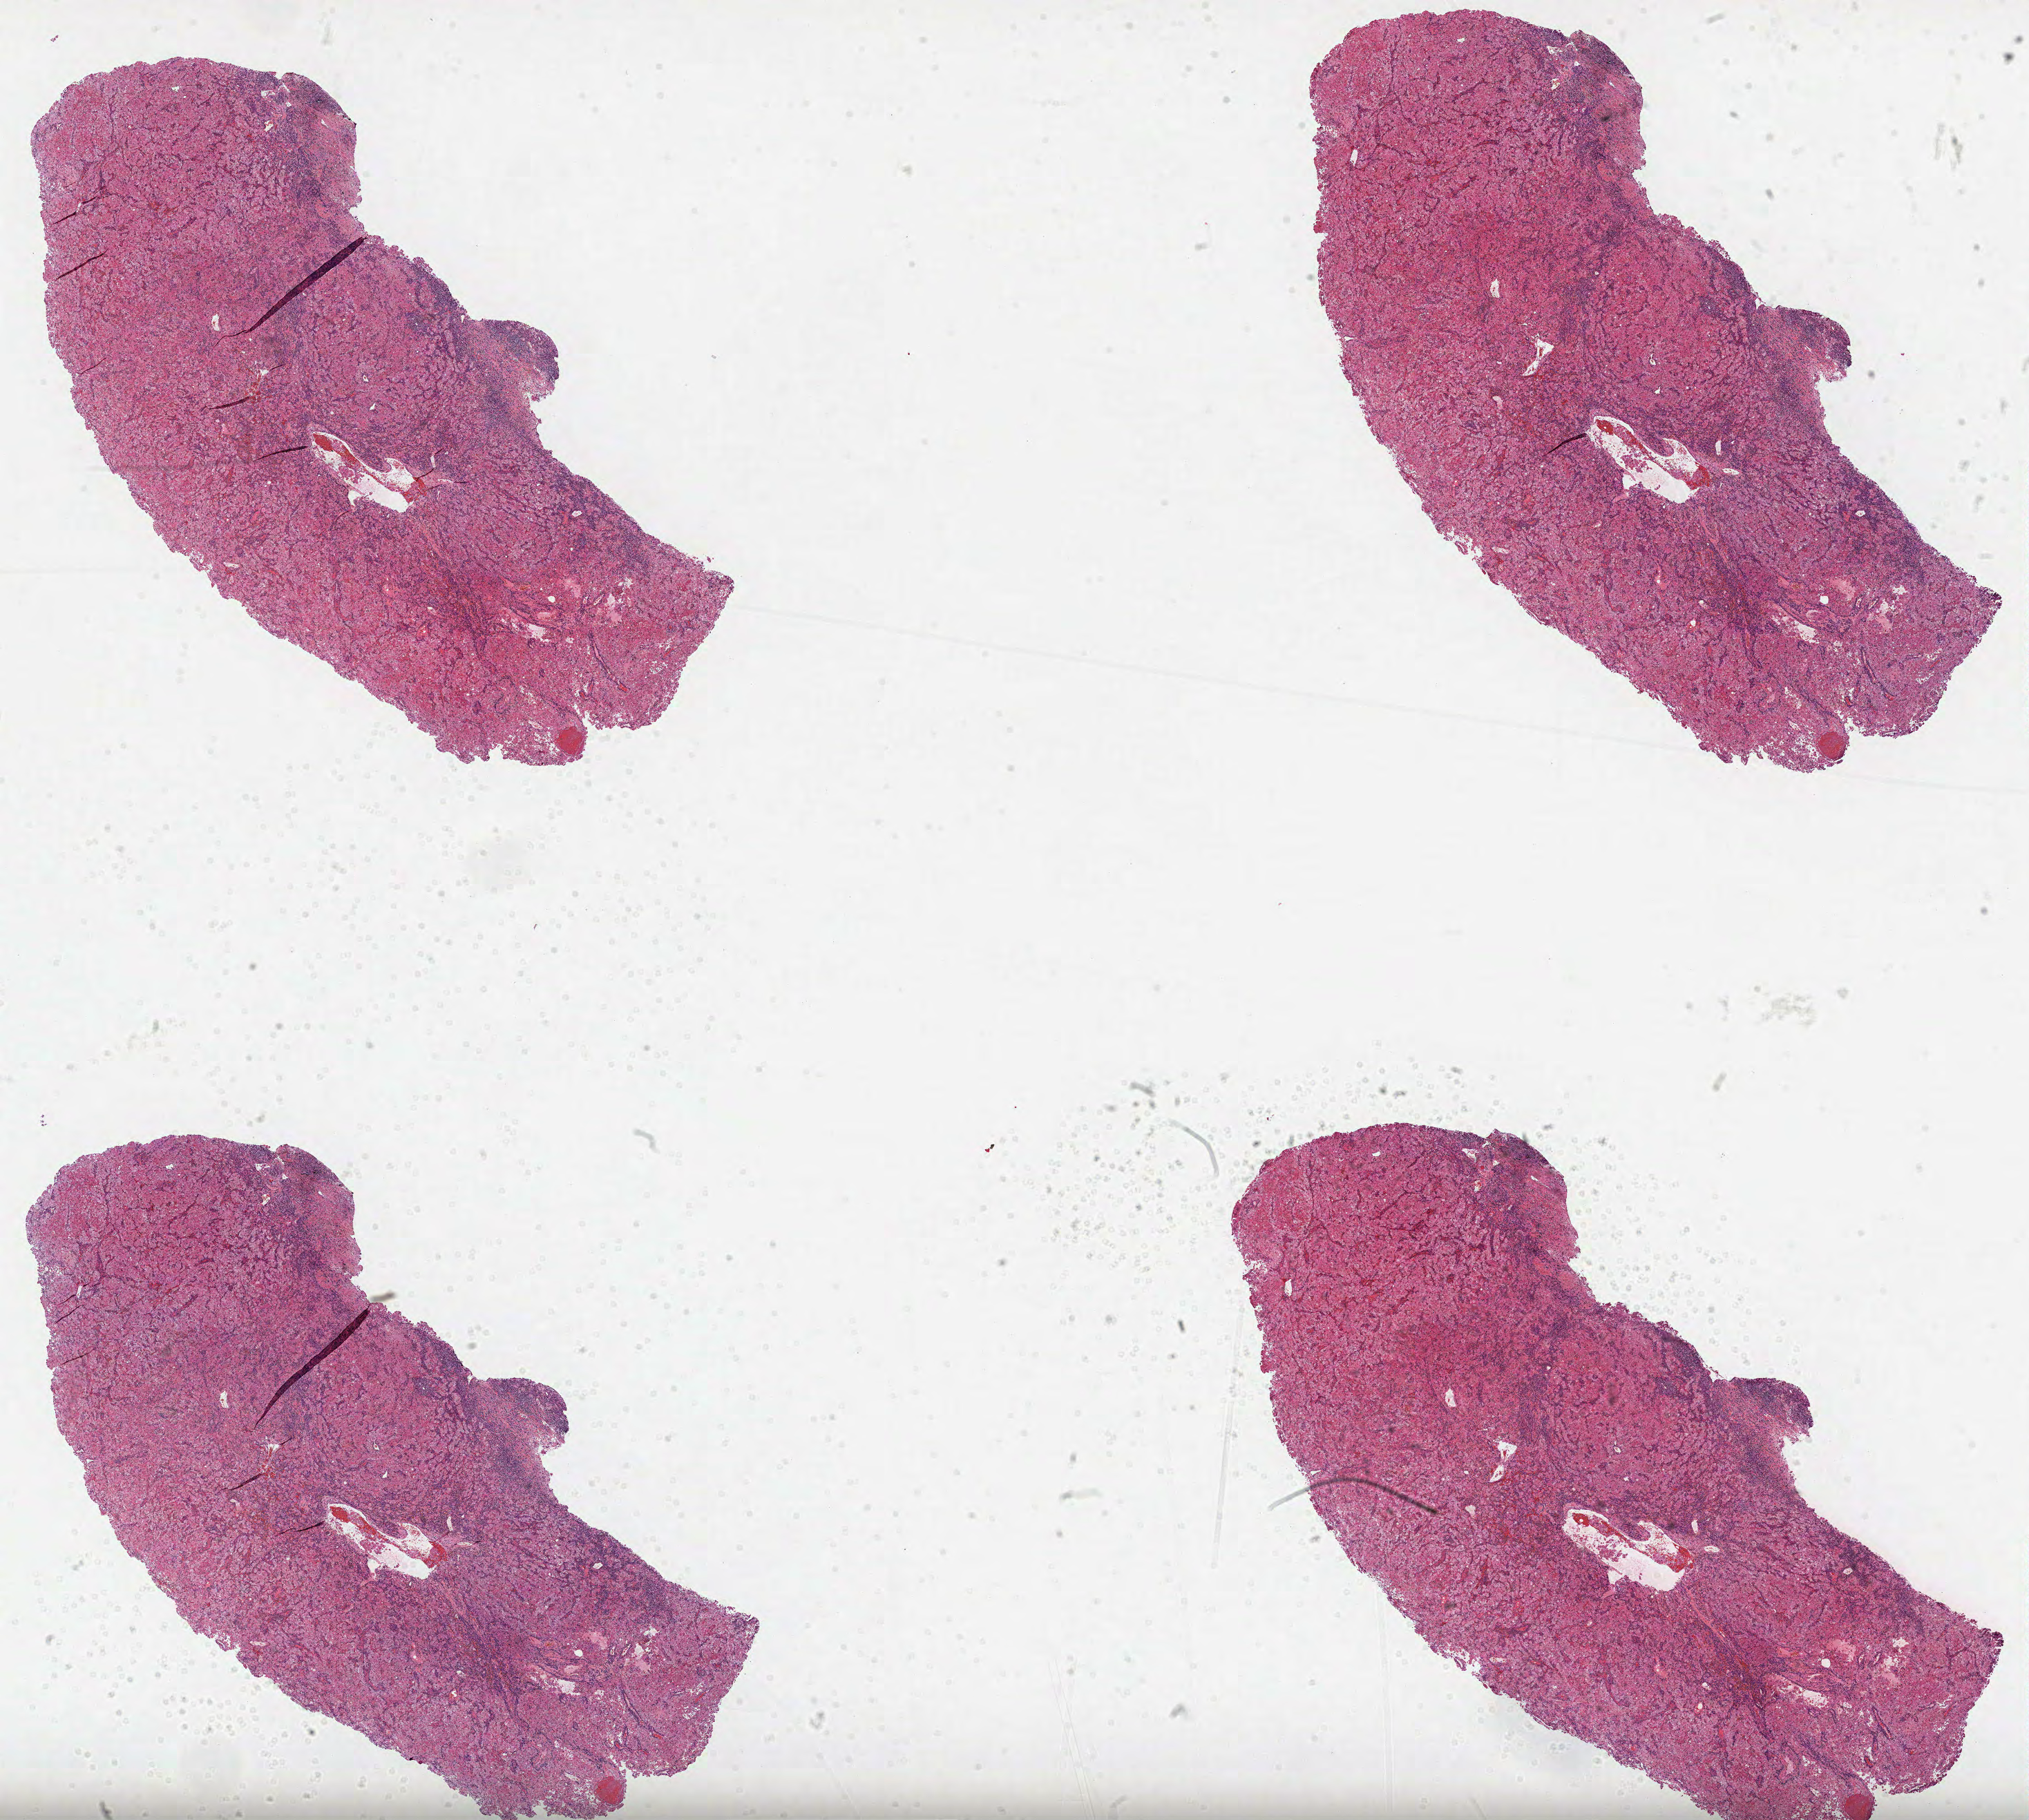
Digitized H&E tissue section (whole slide) — whole scanned area (about 23.7 x 21.3 mm) shown as a low-resolution overview, formalin-fixed paraffin-embedded (FFPE) diagnostic section, sample: primary tumour, kidney. Male patient; age at initial diagnosis 52 years. Histologic grade: G3 (poorly differentiated).
* TNM: T2a NX M0
* diagnosis: Clear cell adenocarcinoma, NOS
* laterality: left
* AJCC pathologic stage: II